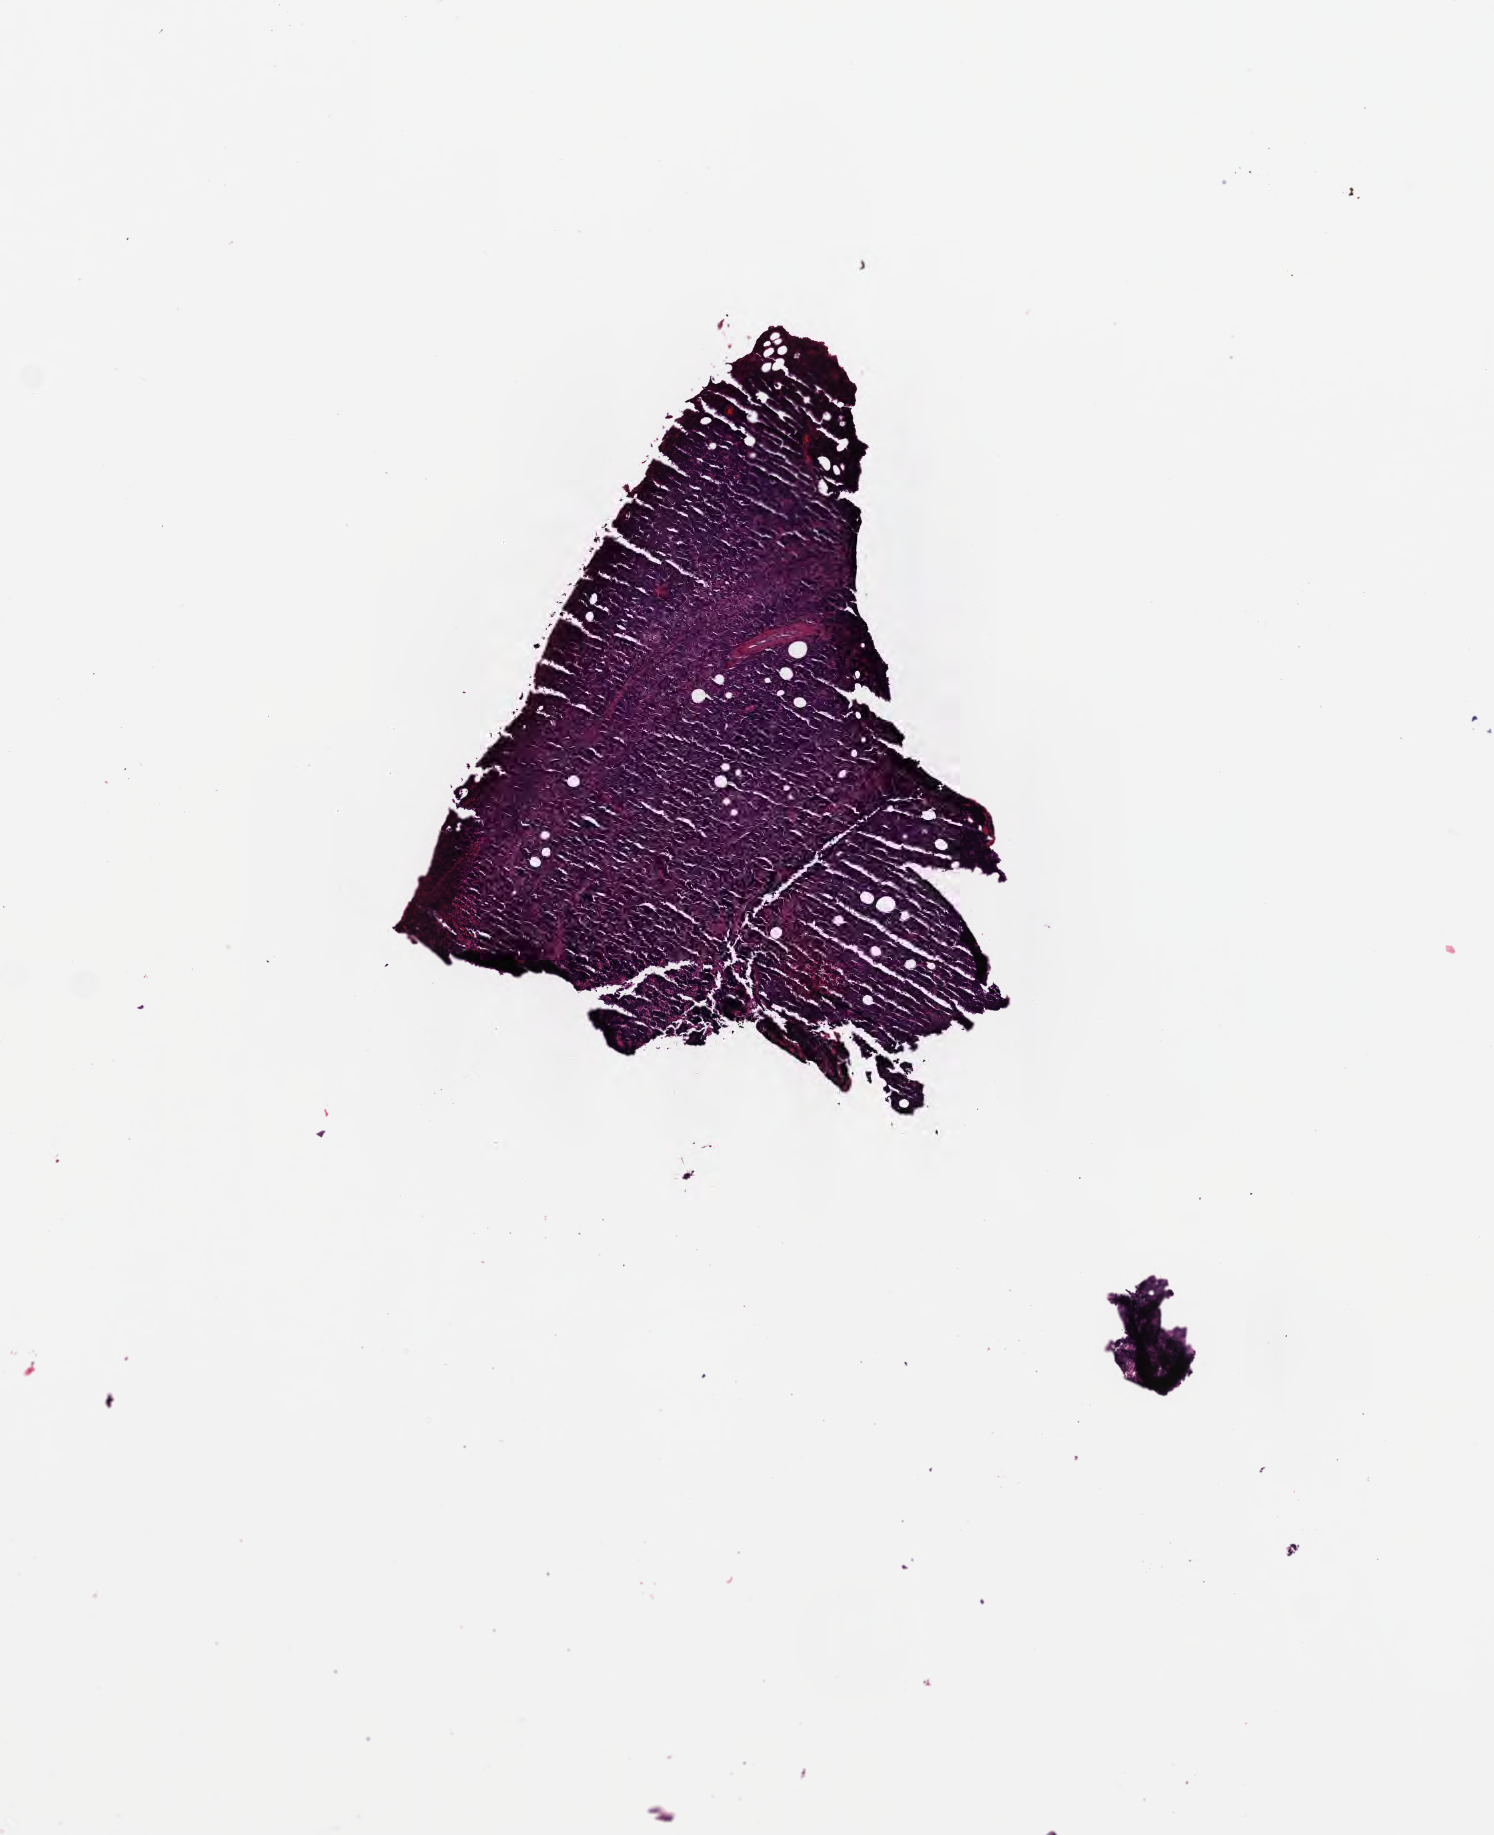
Hematoxylin and eosin (H&E) whole-slide image — shown as a low-resolution overview of the whole scanned area (about 6.0 x 7.4 mm), FFPE section, specimen: primary tumor. Female patient, 40 years old. Slide review estimates, as recorded: tumor cells 90%, tumor nuclei 90%, stromal cells 5%, necrosis 5%, normal cells 0%. Infiltration values recorded for this section: lymphocyte infiltration 5%, monocyte infiltration 20%, neutrophil infiltration 5%.
- diagnosis: Burkitt lymphoma, NOS
- Ann Arbor stage (patient): Stage III